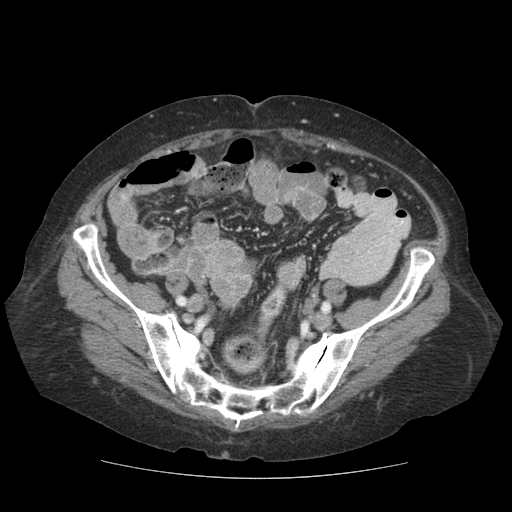
Contrast-enhanced abdominal CT (liver protocol), one axial slice; position 10 of 111 along the scan axis; 140 kVp; soft-tissue window (W 400 / L 40 HU); 2.5 mm slice thickness; 512 × 512 image matrix, field of view 360 × 360 mm. Case-level facts recorded for this patient, not image findings: diagnosis: hepatocellular carcinoma (patient treated with transarterial chemoembolisation; whether this scan precedes or follows treatment is not stated here); TNM stage (as recorded): Stage-I; Child-Pugh class: A; tumour differentiation: moderately-poorly differentiated; tumour nodularity: uninodular.
Outlined on this slice (semi-automatically segmented with operator editing):
- liver parenchyma outside the tumour (the mass and vessels are separate outlines, so this box may not span the whole liver): box from (x=118, y=208) to (x=139, y=252) px